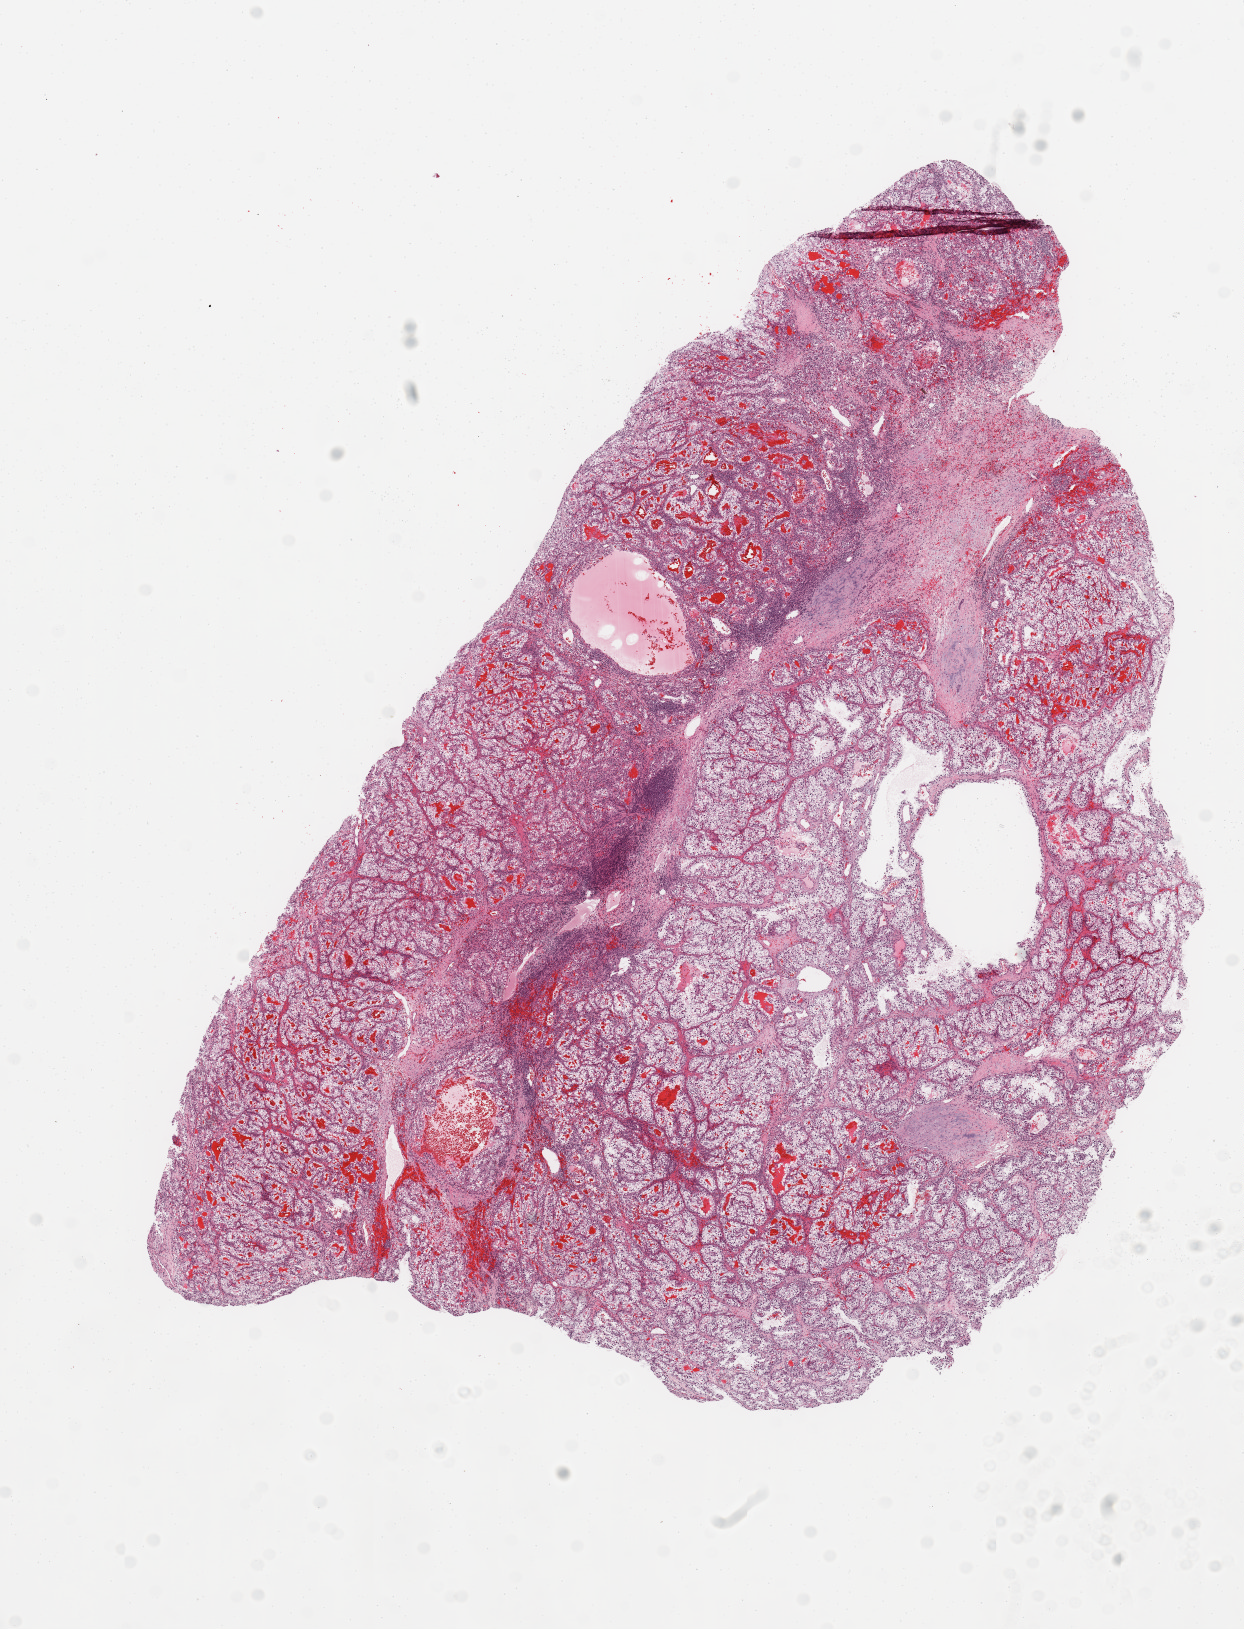
Digitized H&E tissue section (whole slide), low-resolution overview of the scanned area, about 9.8 x 12.9 mm, tumour tissue sample, sampled site: kidney. Patient: male, age 37 years. Histologic grade: G3 (poorly differentiated). Pathologist review of this section (percent, as recorded): tumour nuclei 85%, necrosis 2%.
Histologic diagnosis: Renal cell carcinoma, NOS. AJCC pathologic stage: I. Primary tumour site (as recorded): middle.